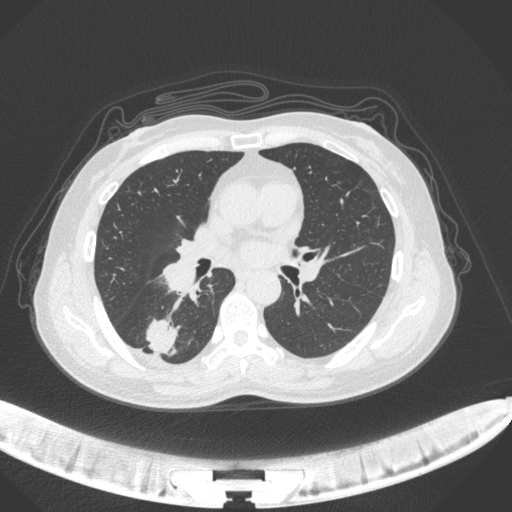
Chest CT, one axial slice; position 163 of 352 along the scan axis; reconstruction kernel B31f; 120 kVp; lung window (W 1500 / L -600 HU); 1 mm slice thickness; 512 × 512 image matrix, field of view 400 × 400 mm. Patient: female, 55 years. From the clinical record (not read from this slice): clinical TNM (as recorded): T1c N1 M0.
Annotated regions visible in this slice (bounding box drawn by a radiologist):
- lung tumour (recorded histology: adenocarcinoma): bounding box [x1, y1, x2, y2] px = [144, 314, 182, 357]